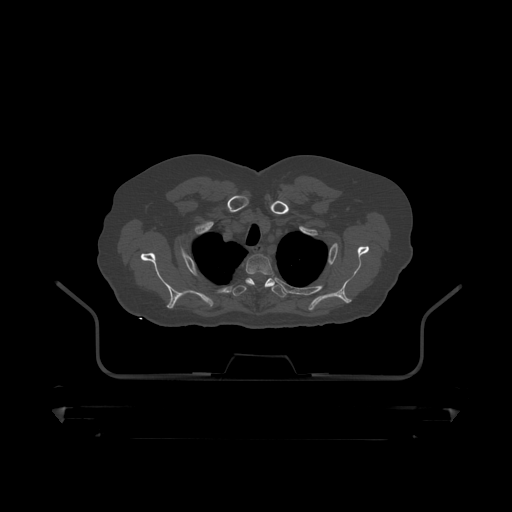
CT including the spine, one axial slice. 120 kVp. Bone window (W 1800 / L 400 HU). 1.25 mm slice thickness. 512 × 512 image matrix, field of view 650 × 650 mm. Patient: male, 60 years. From the clinical record (not read from this slice): primary cancer: prostate.
Outlined on this slice (semi-automatic segmentation, software-assisted and operator-edited):
- T2 vertebra: bounding box [x1, y1, x2, y2] px = [246, 255, 276, 277]
- T3 vertebra: [233, 278, 287, 298]